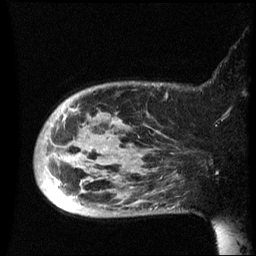
Breast MRI (dynamic contrast-enhanced), one sagittal slice; position 13 of 60 along the scan axis; dynamic contrast-enhanced series, image 2 of 3 at this slice position (ordered by acquisition); 1.5 T; TE 4.2 ms, TR 8.4 ms; 2.5 mm slice thickness; 256 × 256 image matrix. Patient: female, 49 years.
Structures marked on this image (semi-automatically segmented with operator editing):
- analysis volume of interest (the breast-tissue region the enhancement analysis was run in; not a lesion): box from (x=35, y=82) to (x=181, y=217) px
- tumour enhancement mask (voxels above the 70 % enhancement threshold inside the analysis volume of interest): (x=57, y=110)–(x=77, y=185)